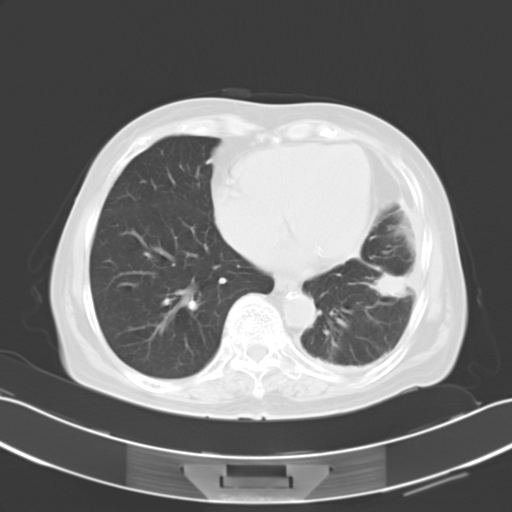
Chest CT, one axial slice; position 11 of 29 along the scan axis; 120 kVp; lung window (W 1500 / L -600 HU); 512 × 512 image matrix, field of view 353 × 353 mm. Patient: female, 82 years. From the clinical record (not read from this slice): clinical TNM (as recorded): T1c N0 M1.
Structures marked on this image (rectangle marked by the reading radiologist):
- lung tumour (recorded histology: adenocarcinoma): bounding box (x1, y1, x2, y2) in pixels: (370, 266, 417, 300)